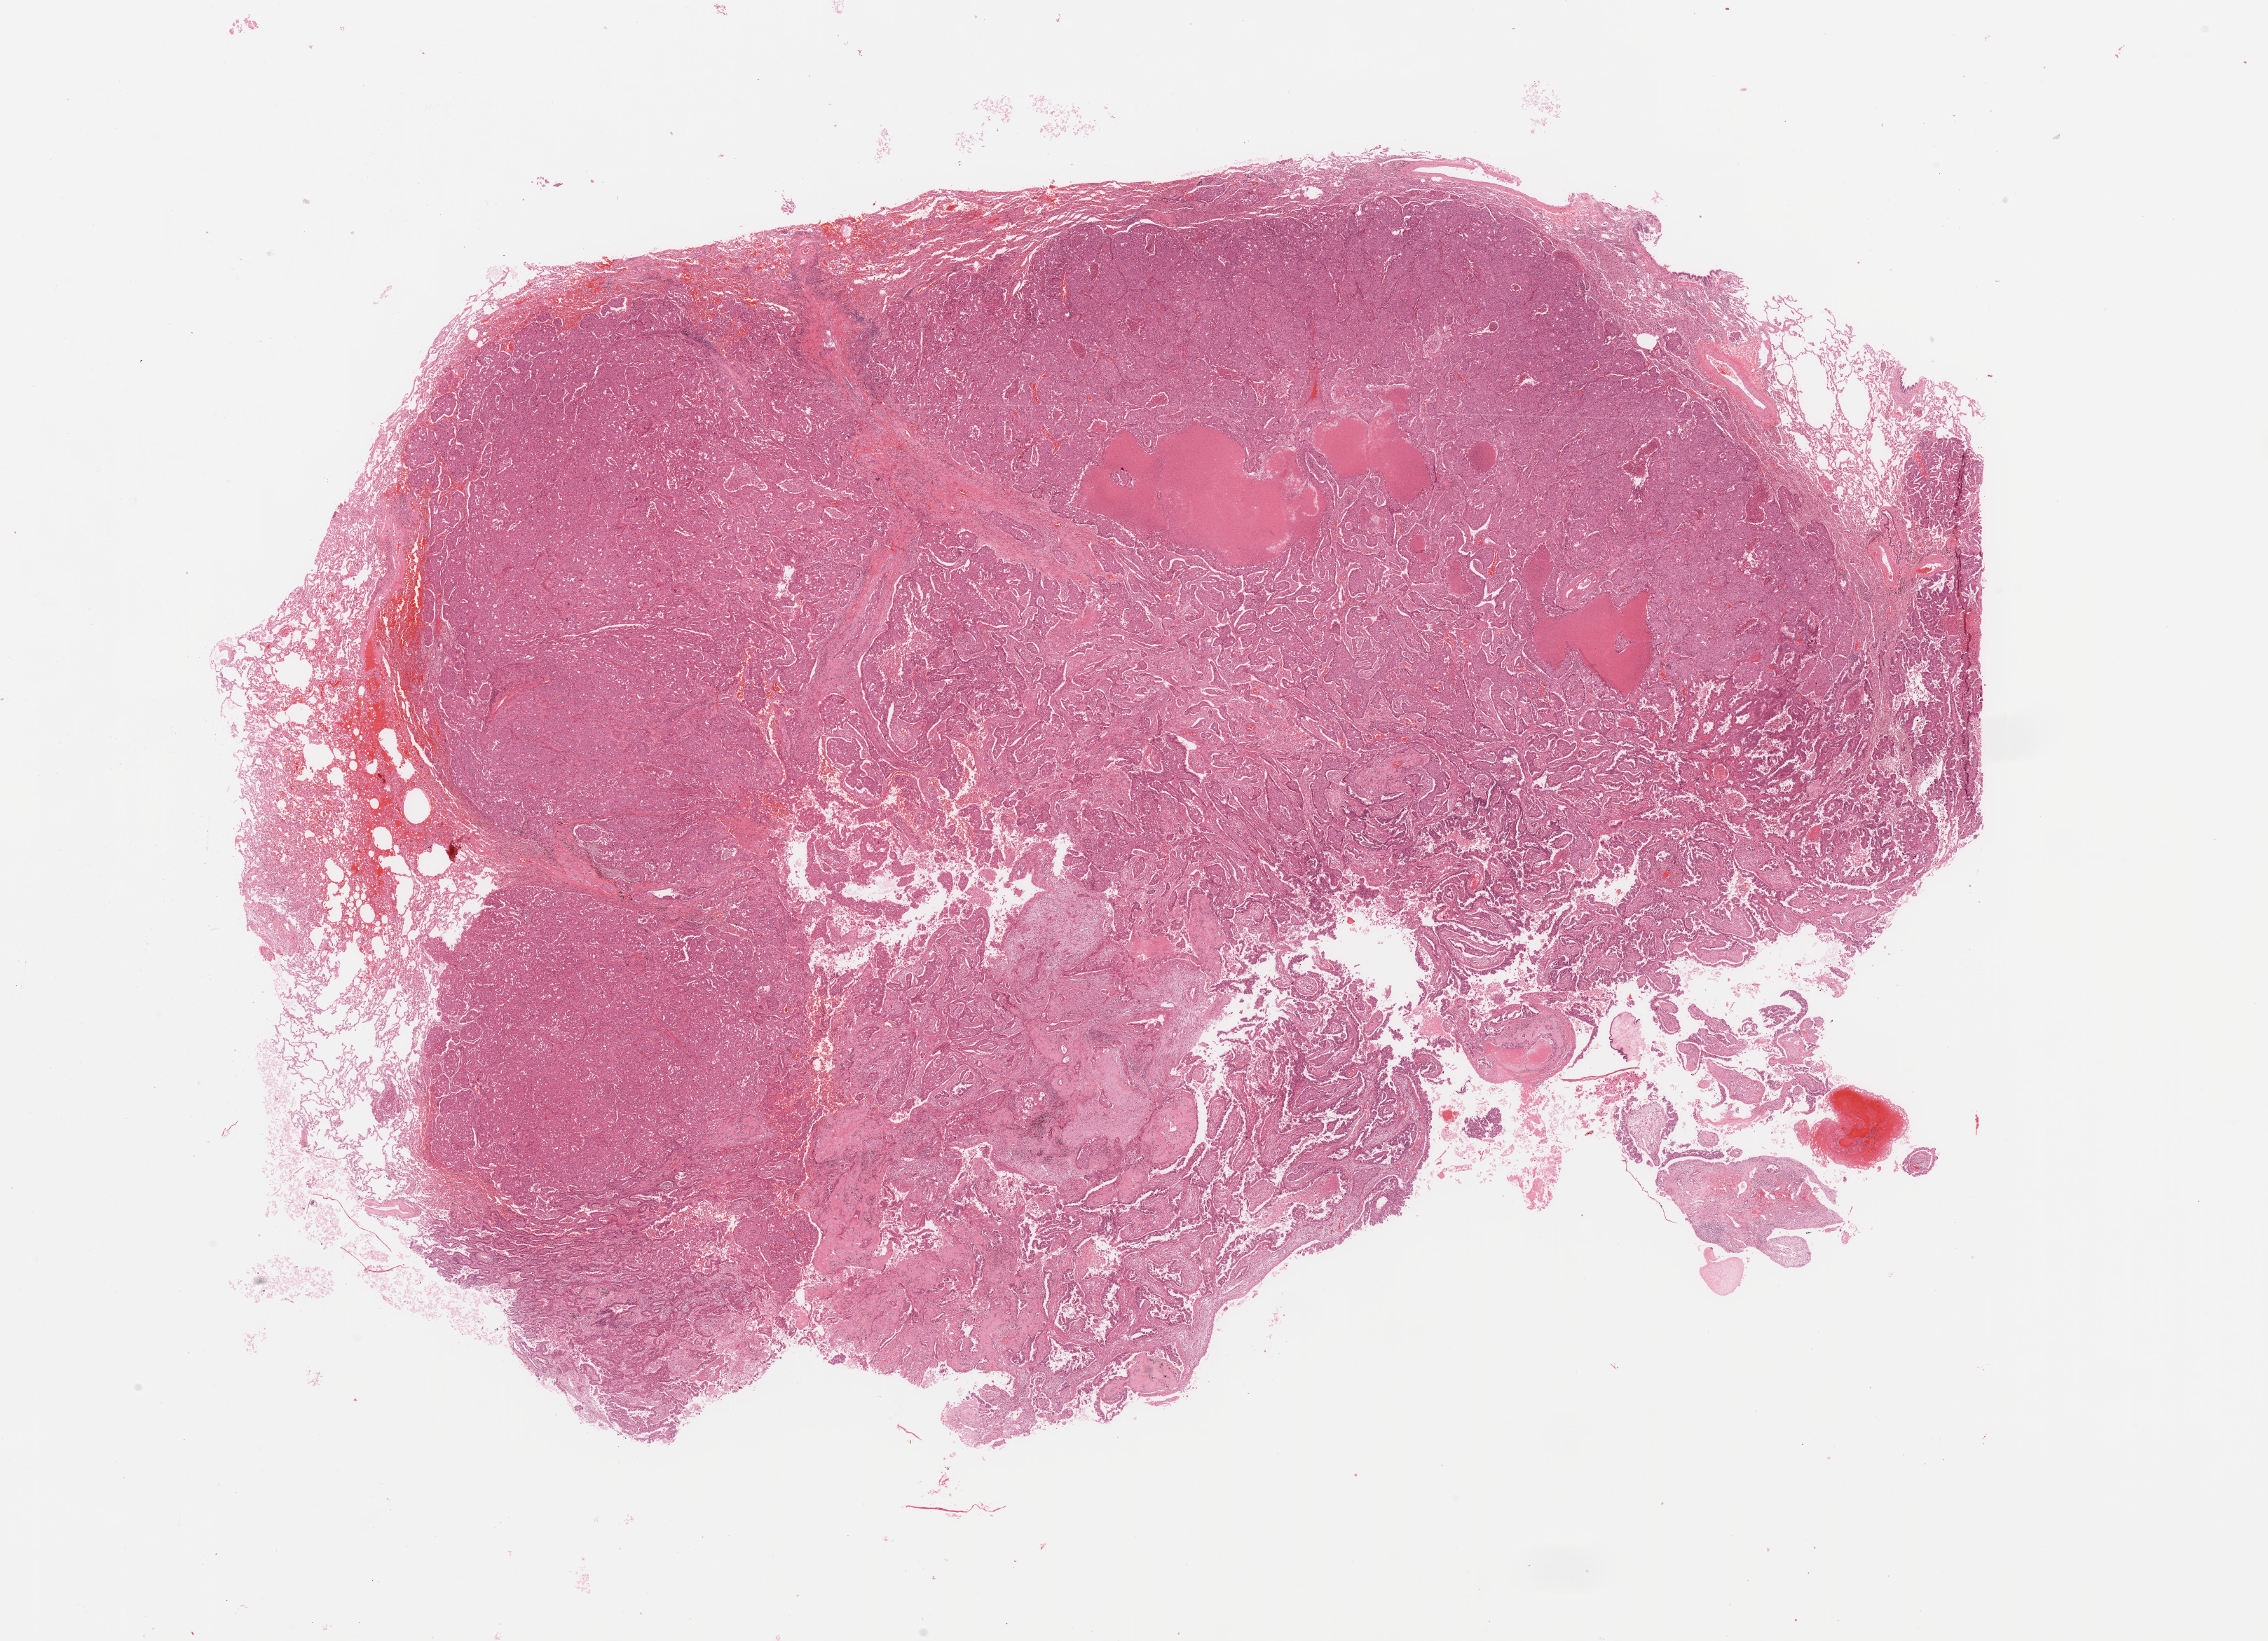
Digitized Hematoxylin and eosin (H&E) stained tissue section (whole slide), shown as a low-resolution overview of the whole scanned area (about 25.6 x 18.5 mm). Lung, tumour tissue. 66-year-old female patient. Histologic grade: G3 (poorly differentiated).
* AJCC pathologic stage: IIB
* histologic diagnosis: Adenocarcinoma, NOS